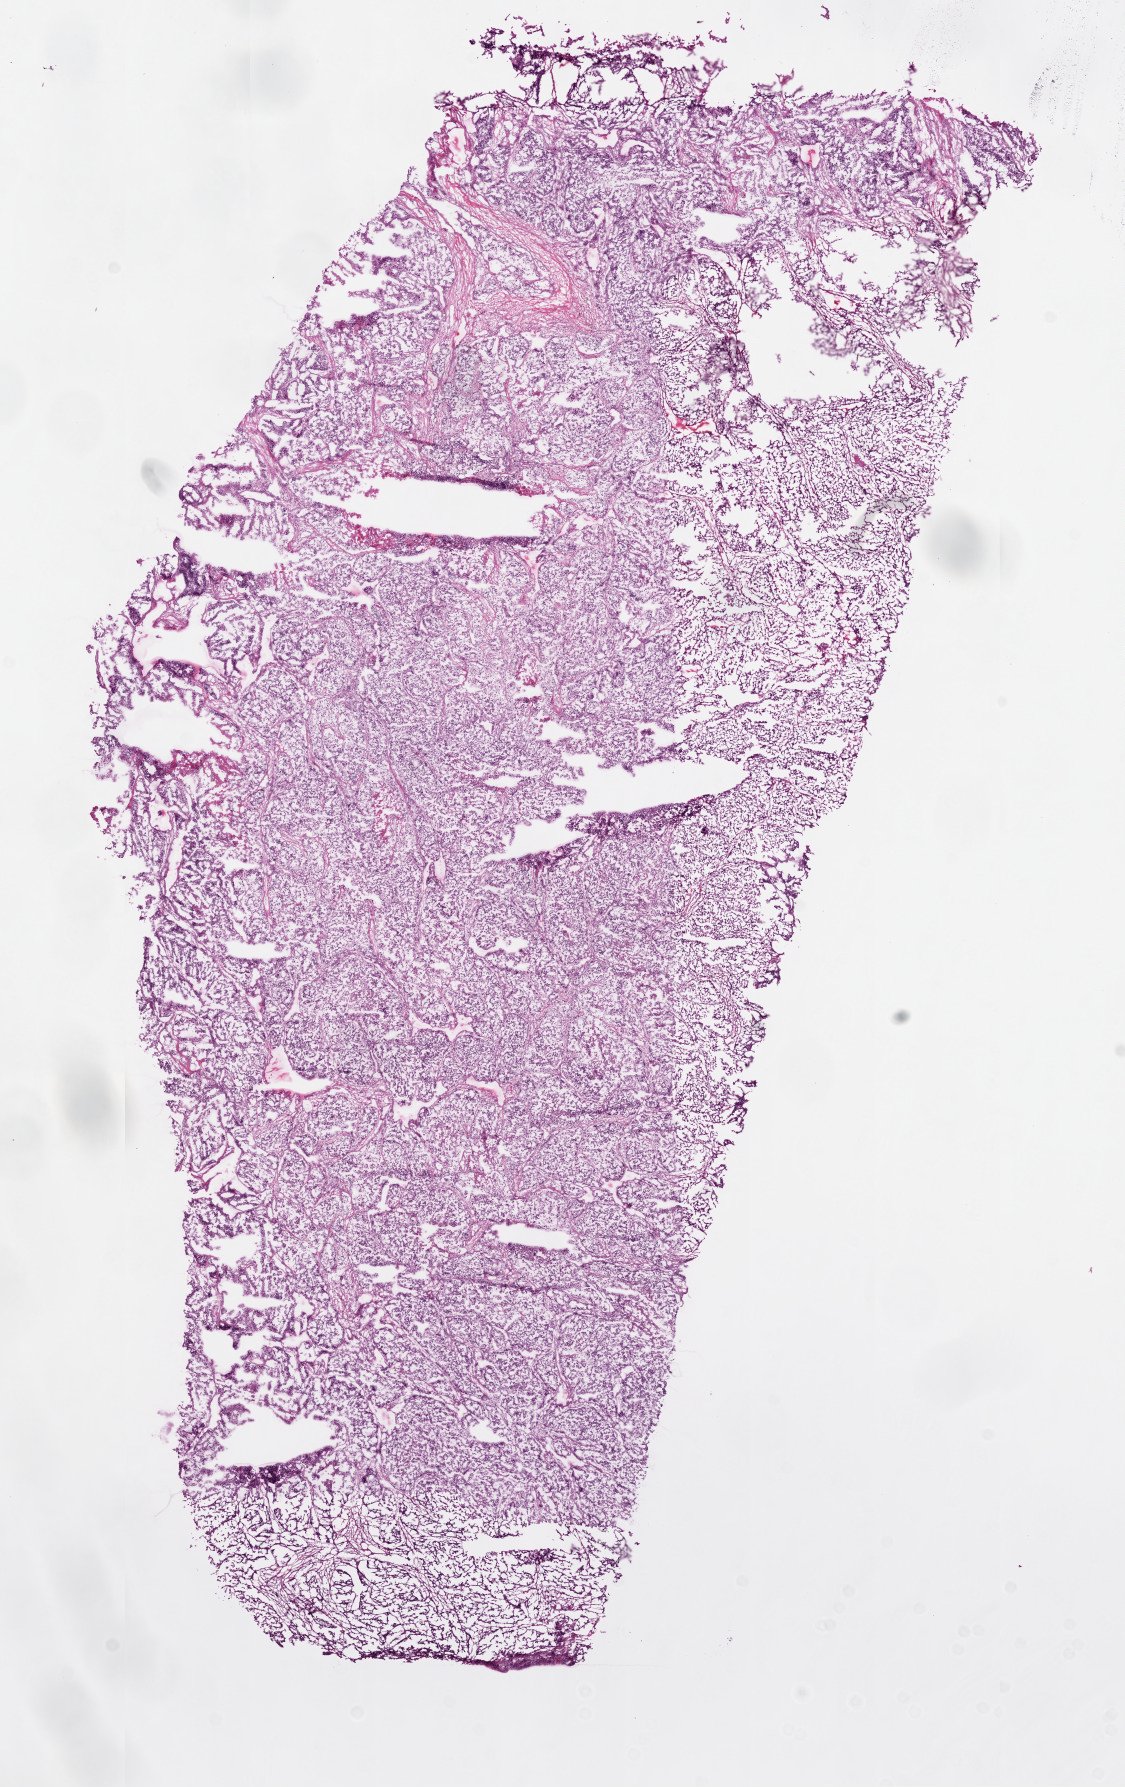
Whole-slide histology image, Hematoxylin and eosin (H&E) stained — shown as a low-resolution overview of the whole scanned area (about 9.0 x 14.3 mm, from a 20x scan). Frozen section from the top of the tissue portion. Sample: primary tumour, lung. Male patient; age at initial diagnosis 60 years. Slide review estimates, as recorded: tumour cells 87%, tumour nuclei 80%, normal cells 0%, stromal cells 10%, necrosis 3%.
TNM: T2 N0 M0. Diagnosis: Adenocarcinoma, NOS (main bronchus). AJCC pathologic stage: IB.